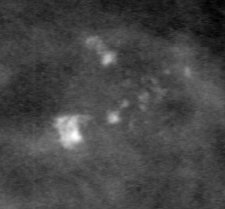
Region of interest cut from a scanned film mammogram (one marked finding), right breast, MLO view, BI-RADS breast density category 3 (scale 1–4).
- Finding: calcifications, morphology dystrophic, distribution clustered; BI-RADS assessment category 3; pathology (as recorded): benign.